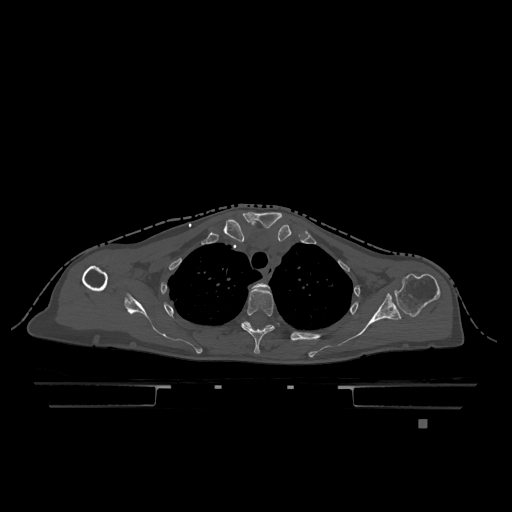
CT including the spine, one axial slice. Slice 918 of 1317 in the series (ordered by position). Bone window (W 1800 / L 400 HU). 0.5 mm slice thickness. 512 × 512 image matrix, field of view 500 × 500 mm. Female patient, age 74 years. From the clinical record (not read from this slice): primary cancer: lung; vertebrae with lytic lesions (as recorded): T1, T4, T5, T6, L4, L5.
Structures marked on this image (semi-automatic segmentation, software-assisted and operator-edited):
- T2 vertebra: box from (x=251, y=282) to (x=270, y=291) px
- T3 vertebra: (x=241, y=287)–(x=275, y=354)
- T4 vertebra: (x=244, y=321)–(x=307, y=341)